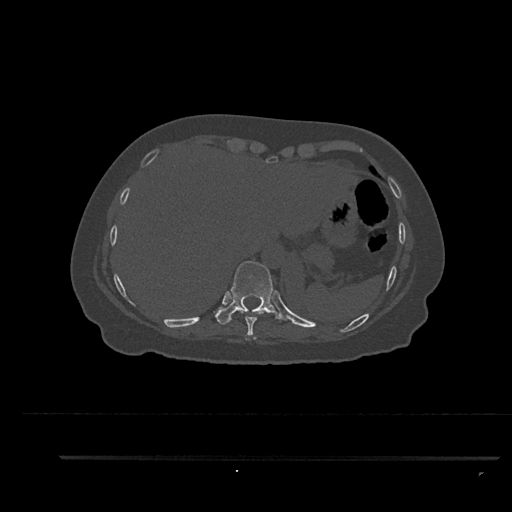
CT including the spine, one axial slice. Reconstruction kernel Br40s/3. Bone window (W 1800 / L 400 HU). 0.5 mm slice thickness. 512 × 512 image matrix. Female patient, age 44 years. From the clinical record (not read from this slice): primary cancer: renal; vertebrae with lytic lesions (as recorded): L1.
Annotated regions visible in this slice (semi-automatic segmentation, software-assisted and operator-edited):
- T10 vertebra: bounding box (x1, y1, x2, y2) in pixels: (215, 261, 284, 325)
- T9 vertebra: (238, 308, 264, 340)